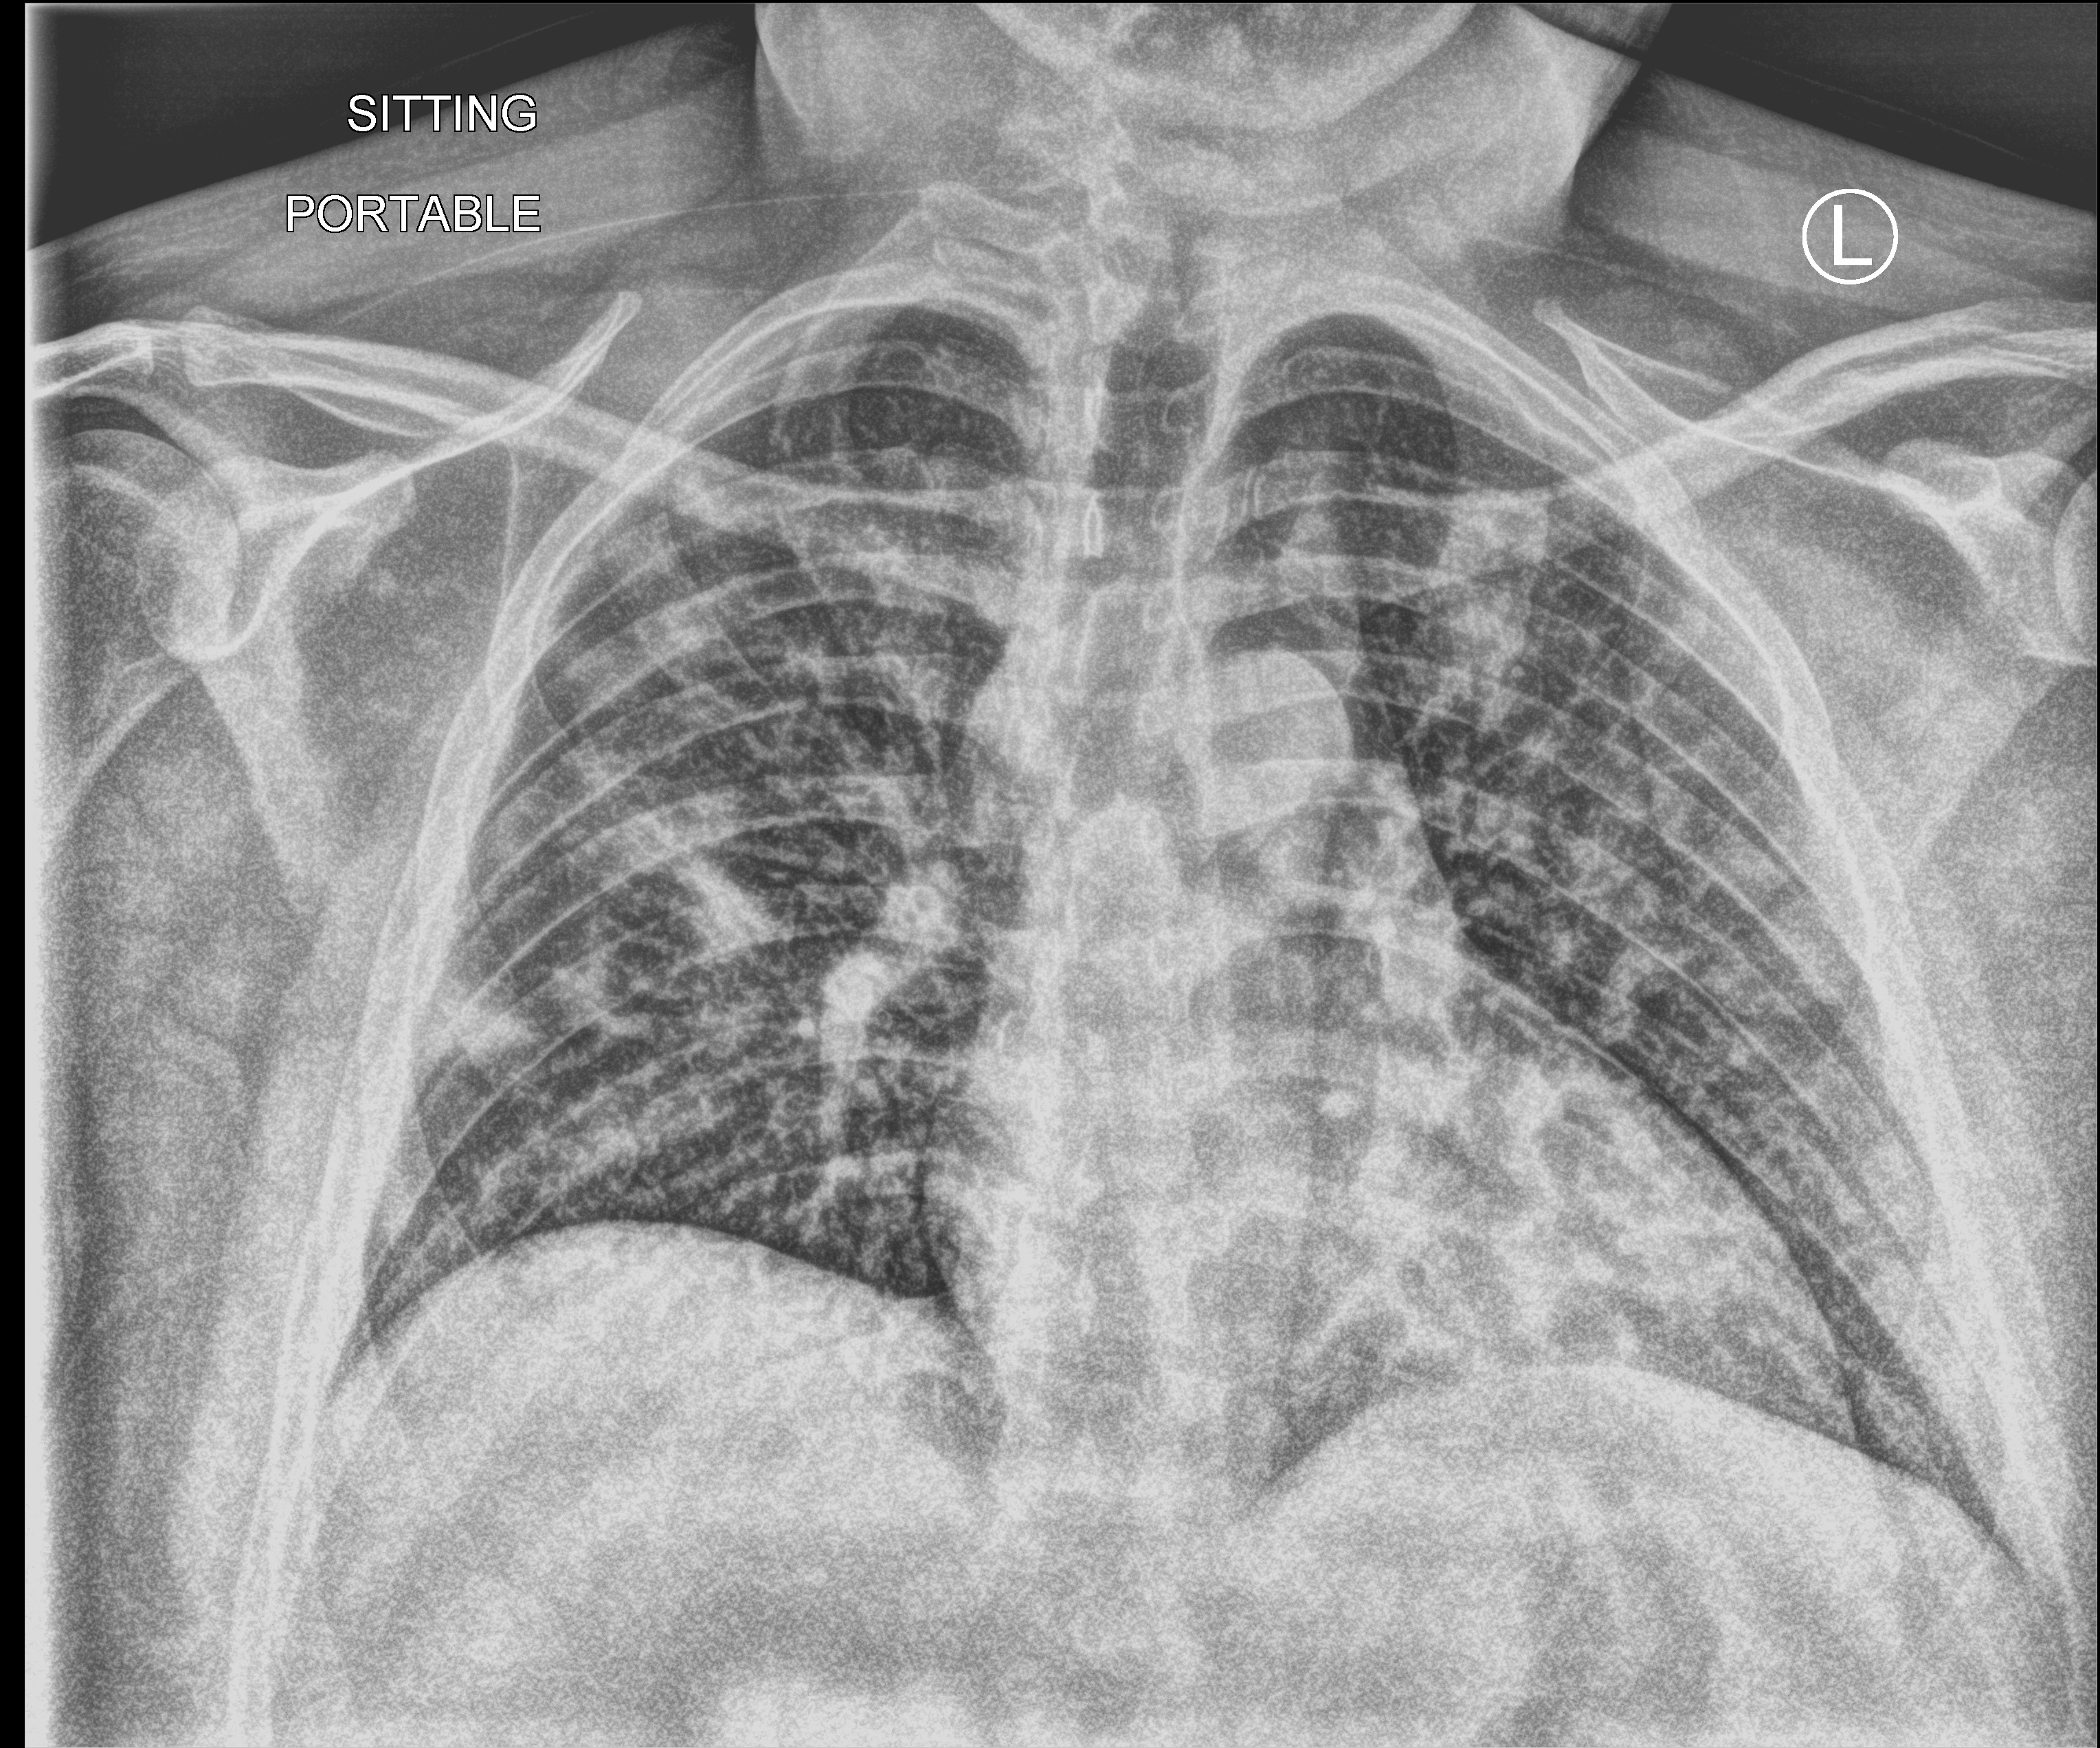
Portable chest radiograph, anteroposterior (AP) projection. Patient hospitalised with COVID-19; male, aged 18–59 years.
Hospital-stay facts (about this admission, not read from this image; timing relative to this image not recorded): mechanically ventilated during this hospital stay: no; diabetes (admission record): no.